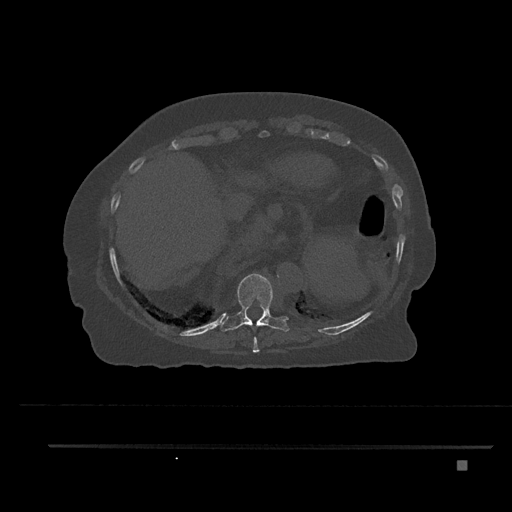
CT including the spine, one axial slice. Slice 361 of 797 in the series (ordered by position). 120 kVp. Bone window (W 1800 / L 400 HU). 0.5 mm slice thickness. 512 × 512 image matrix, field of view 437 × 437 mm. Patient: female, 76 years. Case-level facts recorded for this patient, not image findings: primary cancer: lung.
Annotated regions visible in this slice (semi-automatic segmentation, software-assisted and operator-edited):
- T10 vertebra: bounding box <220,273,290,332> (left, top, right, bottom; pixels)
- T9 vertebra: <253,336,260,353>